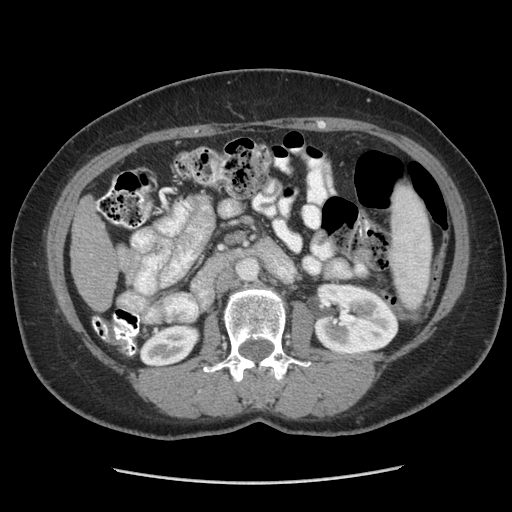
Contrast-enhanced abdominal CT (liver protocol), one axial slice. Slice 119 of 185 in the series (ordered by position). Reconstruction kernel STANDARD. 140 kVp. Soft-tissue window (W 400 / L 40 HU). 512 × 512 image matrix, field of view 360 × 360 mm. Case-level facts recorded for this patient, not image findings: diagnosis: hepatocellular carcinoma (patient treated with transarterial chemoembolisation; whether this scan precedes or follows treatment is not stated here); TNM stage (as recorded): Stage-I.
Outlined on this slice (semi-automatic segmentation, software-assisted and operator-edited):
- liver parenchyma outside the tumour (the mass and vessels are separate outlines, so this box may not span the whole liver): bounding box [x1, y1, x2, y2] px = [70, 196, 118, 310]